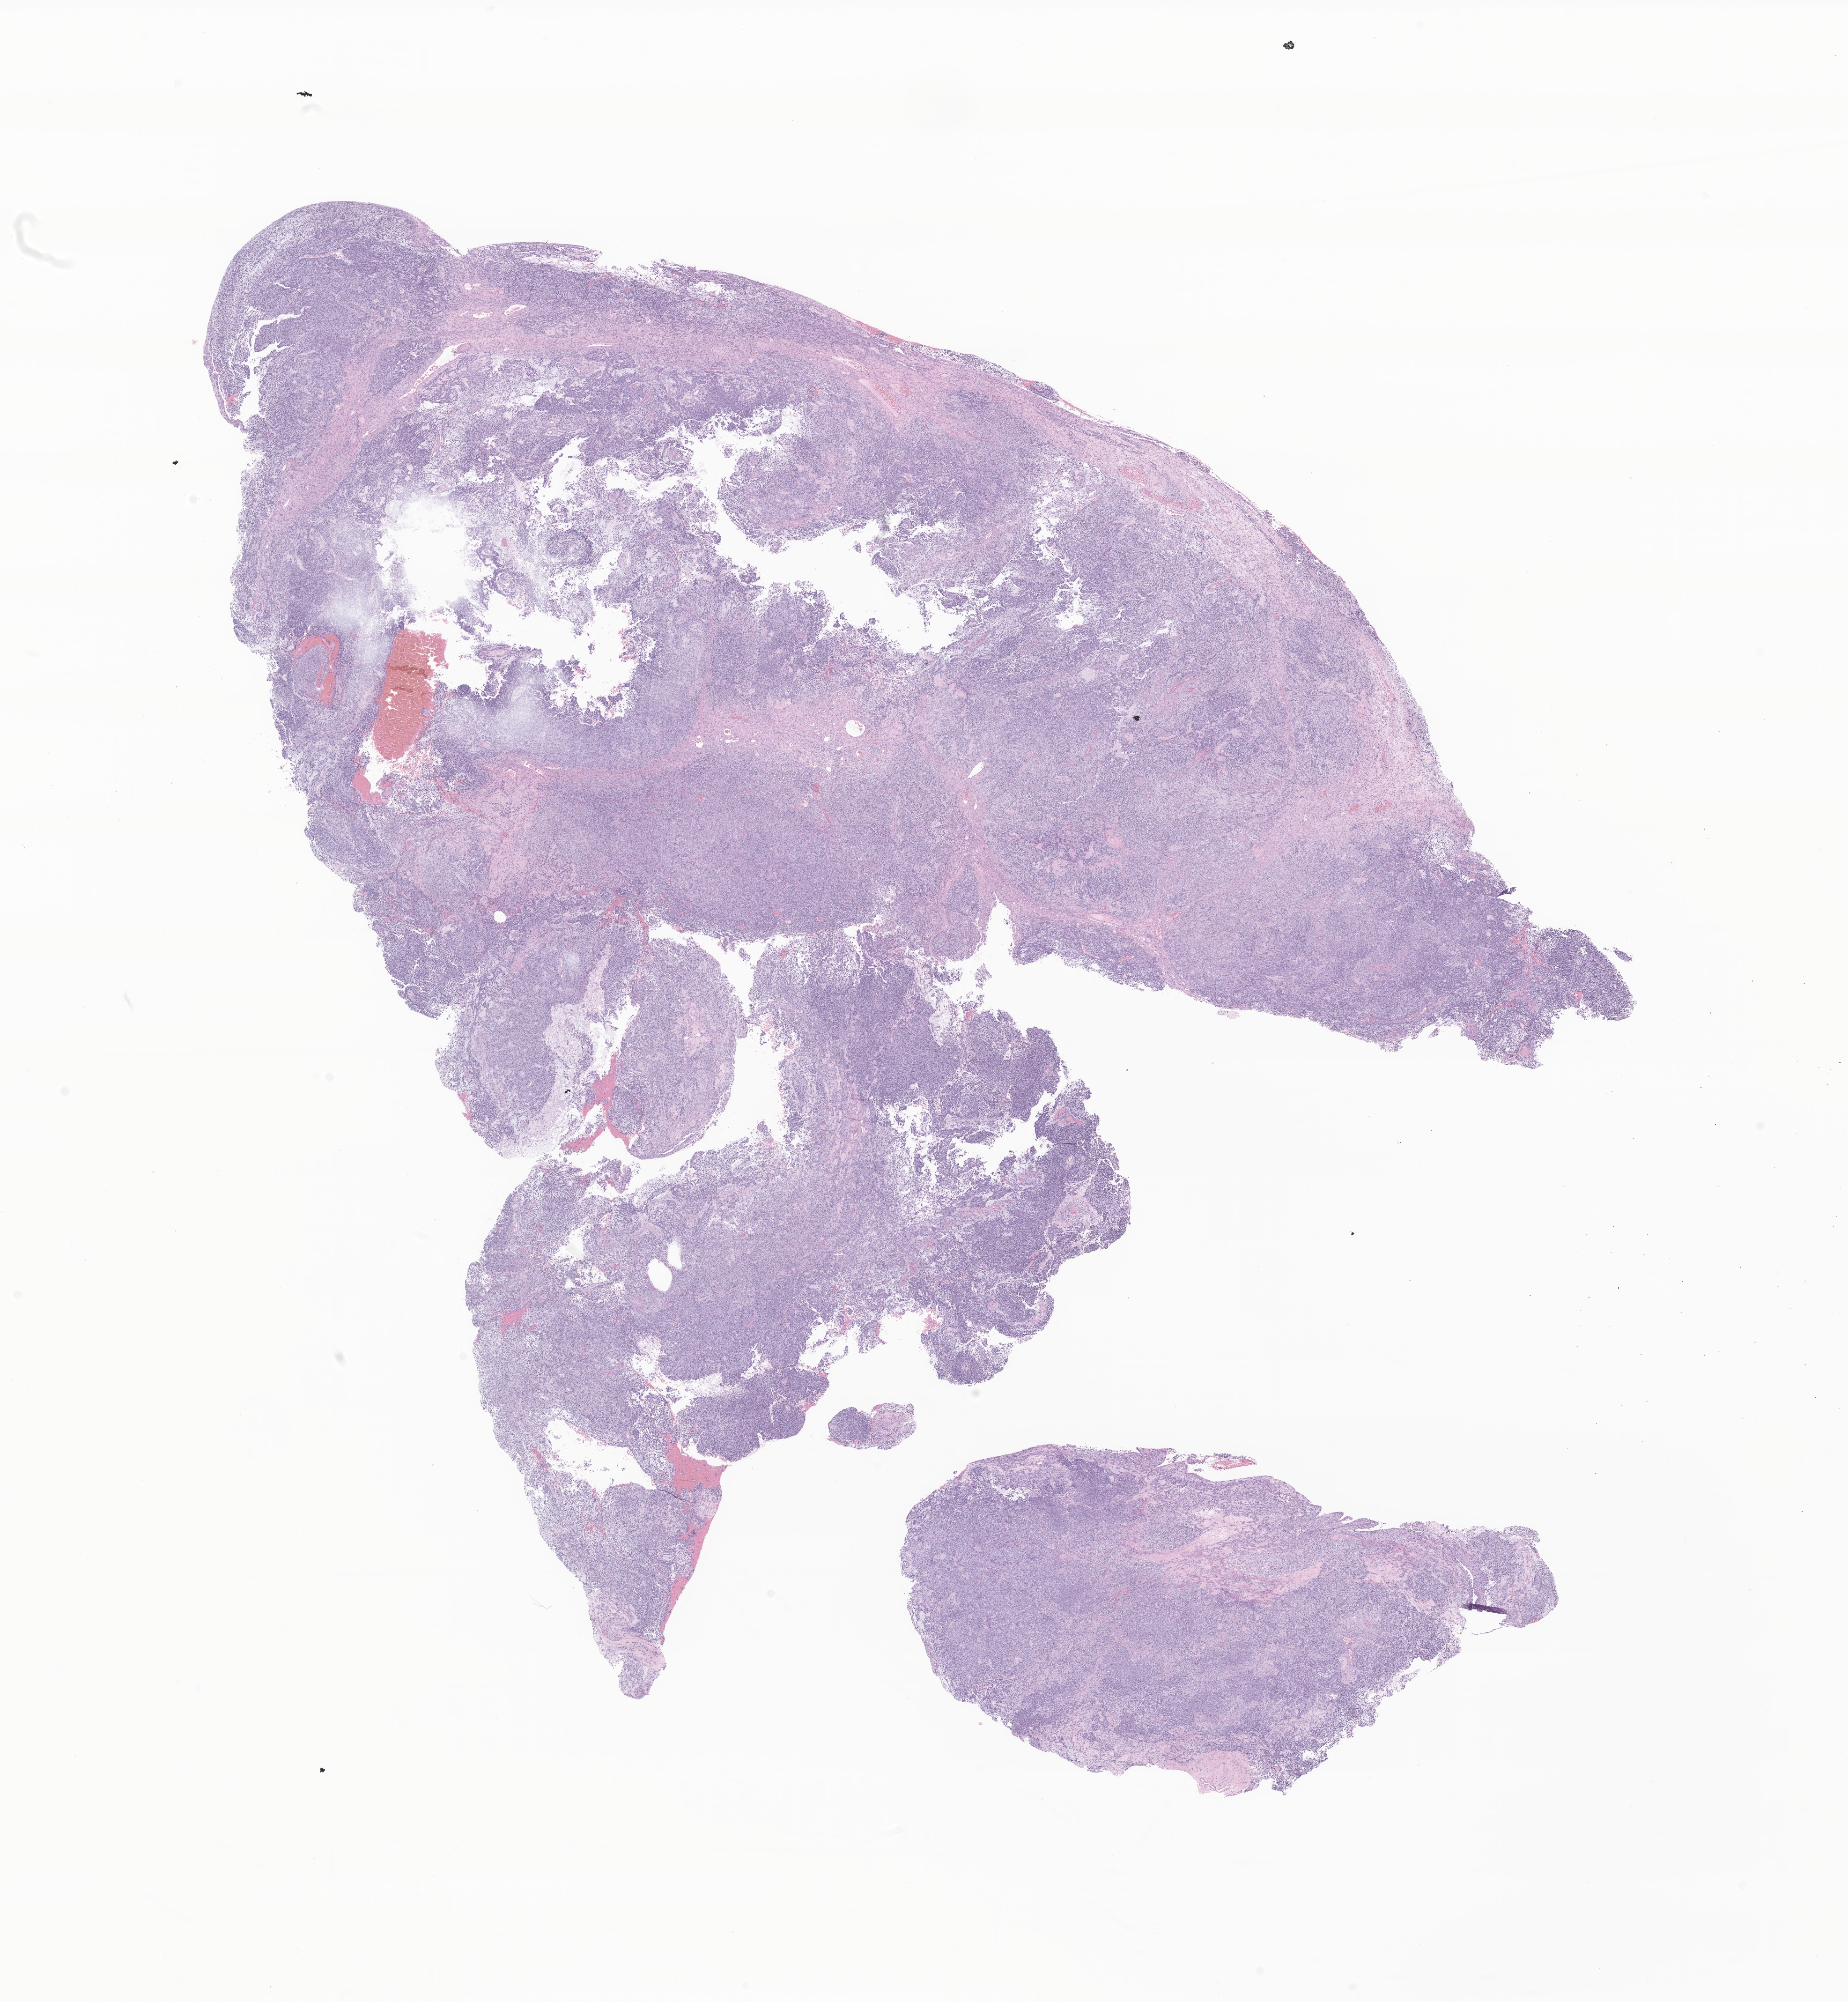
Haematoxylin and eosin whole-slide image of tumor tissue from the brain, shown as a low-resolution overview of the whole scanned area (about 16.6 x 18.0 mm); formalin-fixed, paraffin-embedded (FFPE) tissue. Patient: male, age 617 days (about 1.7 years).
Recorded diagnosis: Neoplasm, malignant.